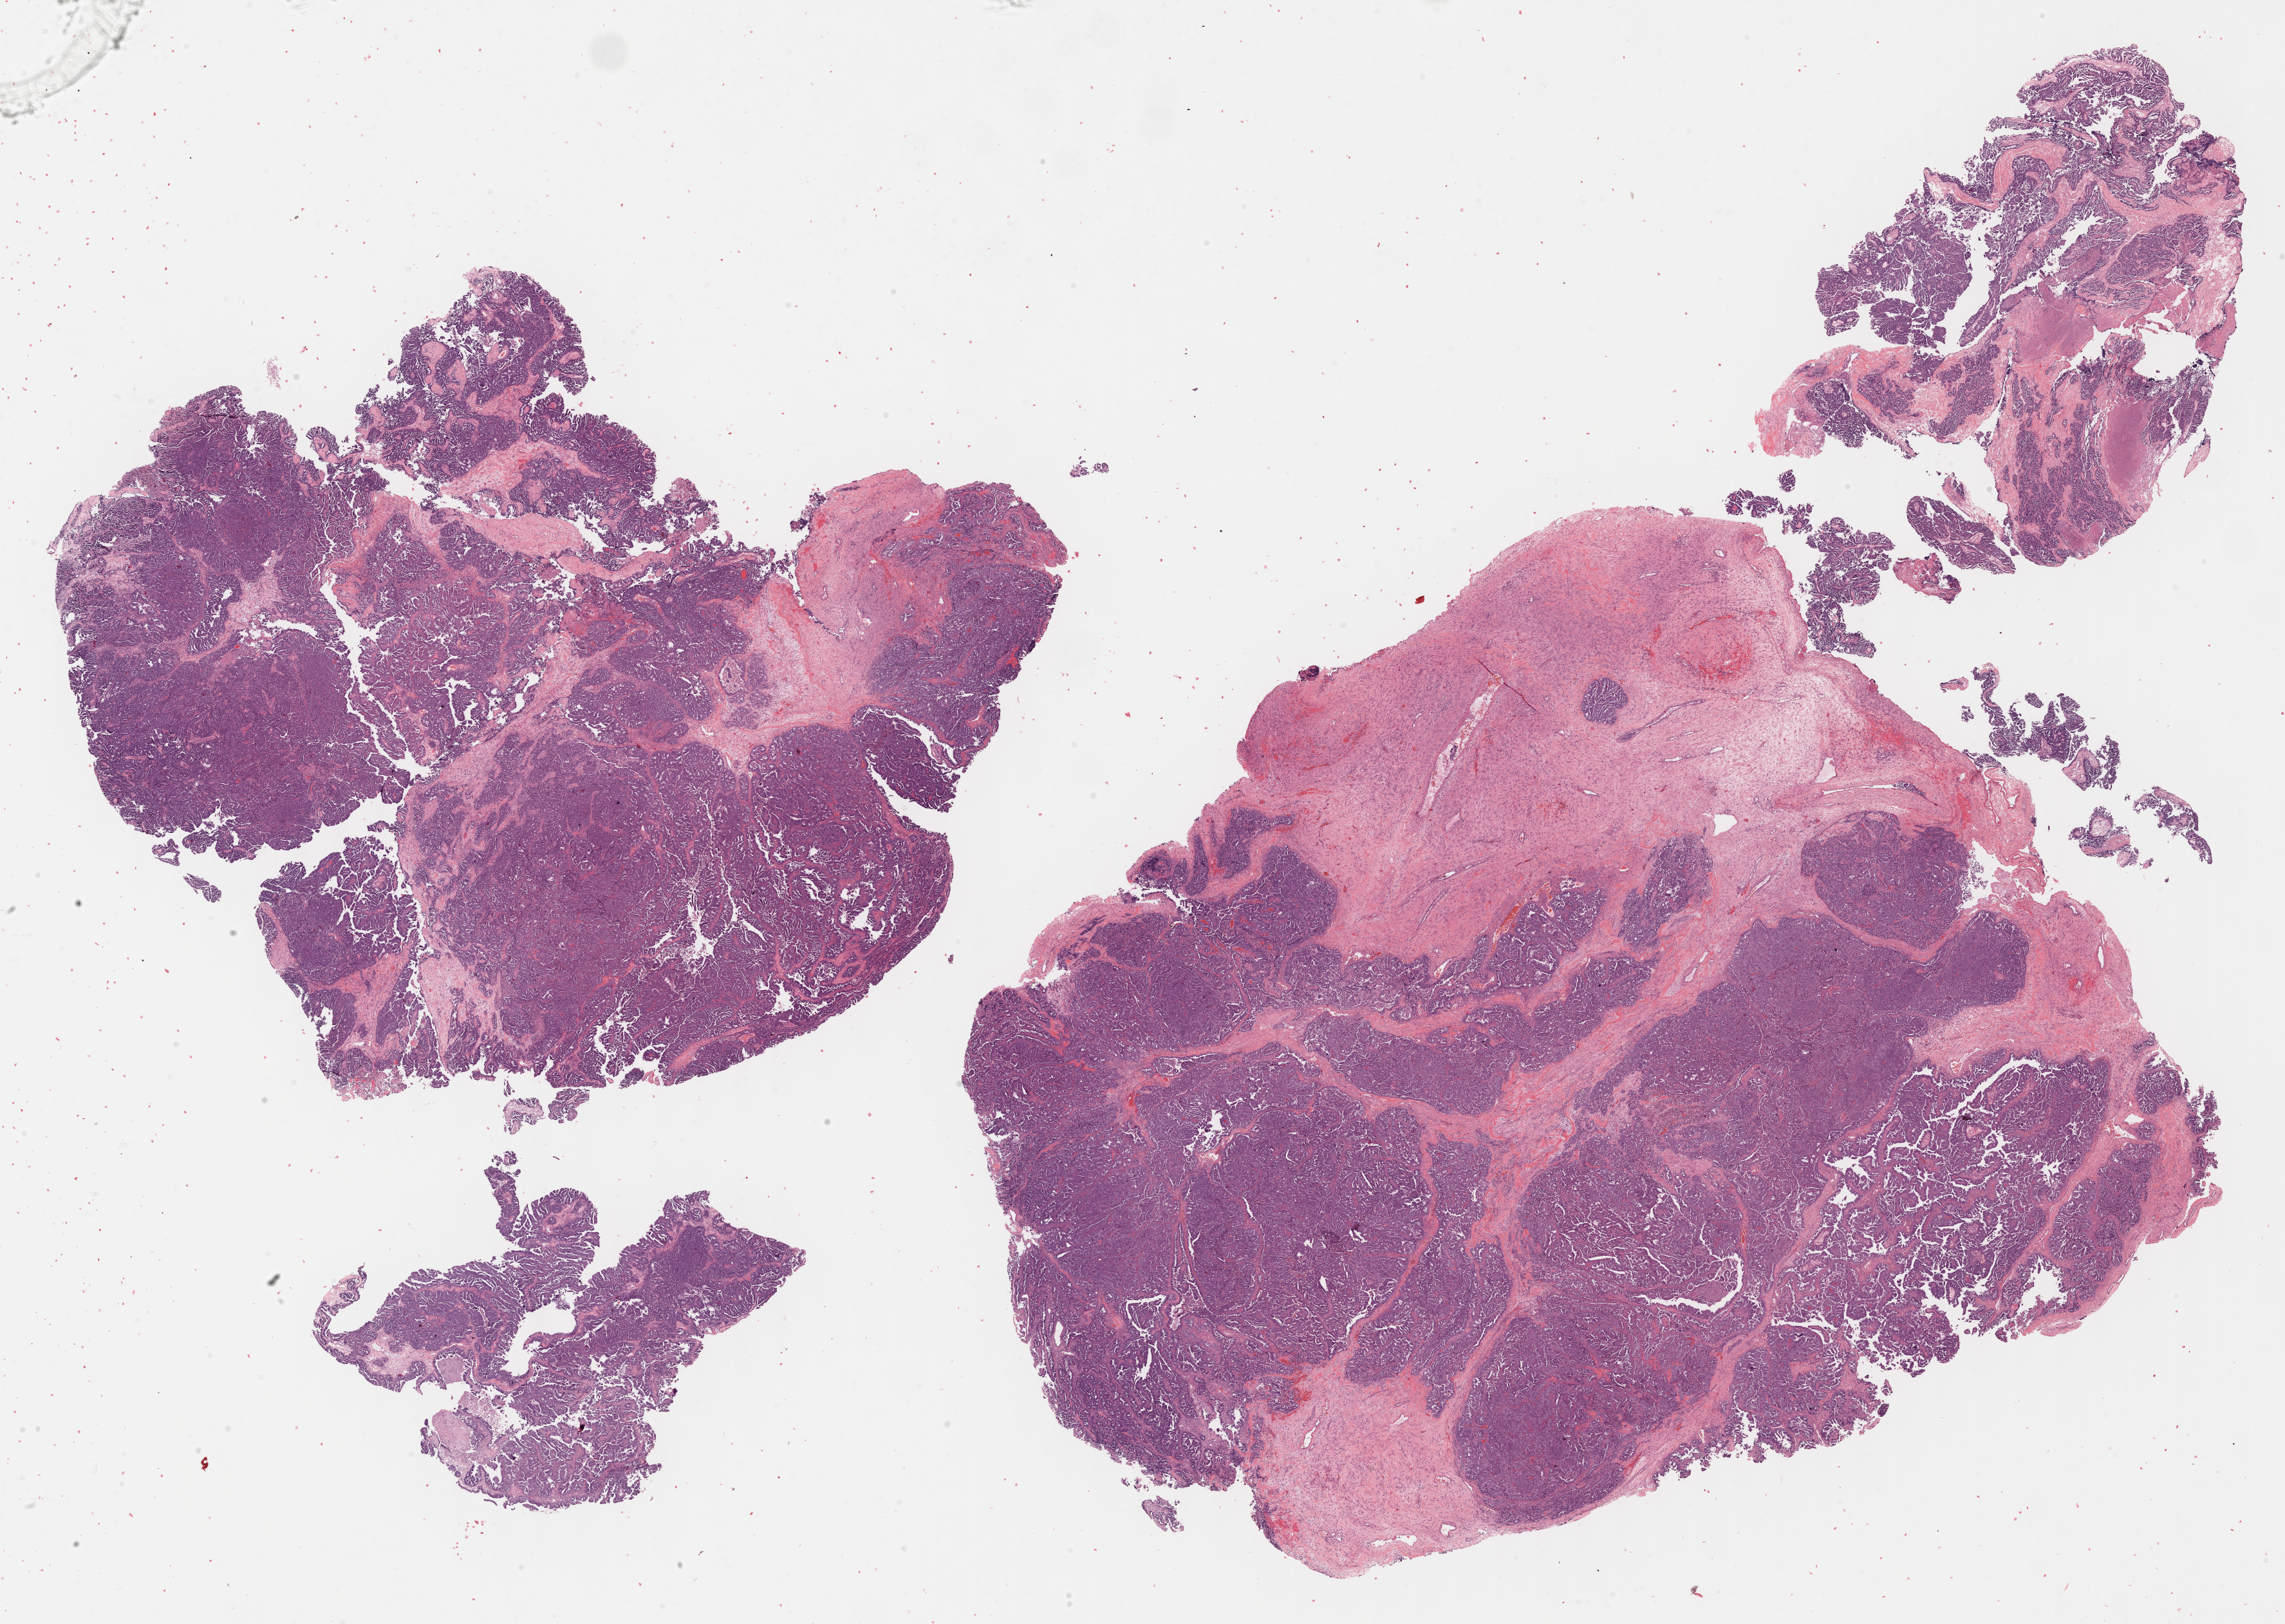
Hematoxylin and eosin (H&E) stained whole-slide image — a low-resolution overview of the entire scanned area, about 28.7 x 20.4 mm (acquisition: 40x scan), formalin-fixed paraffin-embedded (FFPE) diagnostic section, ovary, primary tumour sample. Female patient; age at initial diagnosis 71 years.
Pathologic diagnosis: Serous cystadenocarcinoma, NOS.